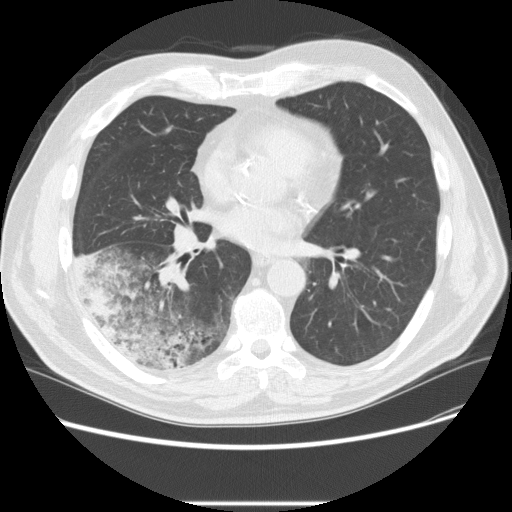
Low-dose screening chest CT, one axial slice; reconstruction kernel STANDARD; lung window (W 1500 / L -600 HU); 2.5 mm slice thickness; 512 × 512 image matrix.
Structures marked on this image (outlined manually by an expert reader):
- lesion 3 (tumor, lower lobe of right lung): bounding box <75,254,131,349> (left, top, right, bottom; pixels)